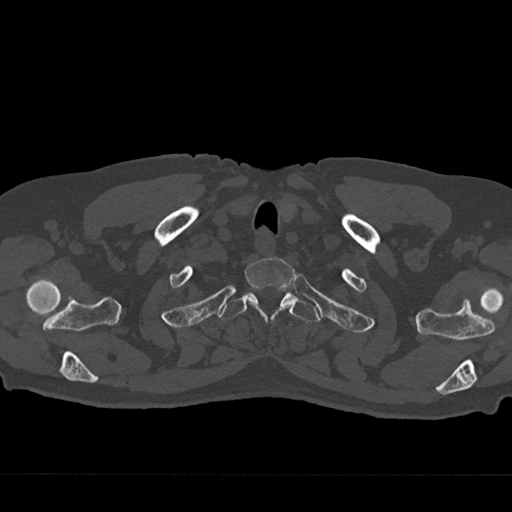
CT including the spine, one axial slice; slice 634 of 797 in the series (ordered by position); 120 kVp; bone window (W 1800 / L 400 HU); 0.5 mm slice thickness; 512 × 512 image matrix, field of view 377 × 377 mm. Male patient, age 75 years. Case-level facts recorded for this patient, not image findings: primary cancer: renal; vertebrae with lytic lesions (as recorded): T4.
Outlined on this slice (semi-automatic segmentation, software-assisted and operator-edited):
- T1 vertebra: bounding box [x1, y1, x2, y2] px = [245, 258, 295, 321]
- T2 vertebra: [219, 289, 320, 323]